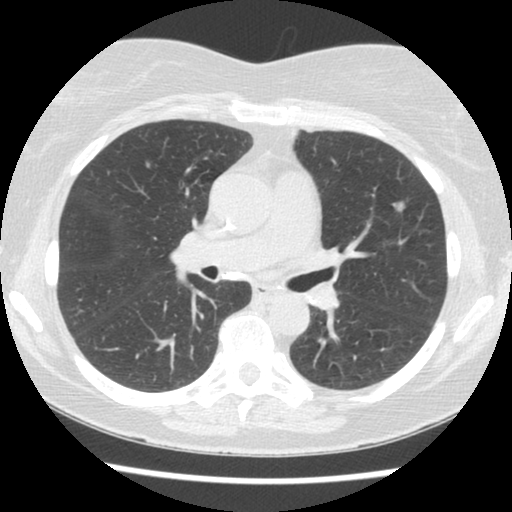
Low-dose screening chest CT, axial slice. Second screening round (one year after baseline). Lung window (W 1500 / L -600 HU). 2.5 mm slice thickness. Standard (soft-tissue) reconstruction kernel (STANDARD). Female, age 60 years at enrolment. Current smoker at enrolment.
Lesion marked by an expert reader, box from (x=376, y=193) to (x=421, y=226) px. The screening reader recorded 3 non-calcified nodules or masses ≥4 mm on this exam (left upper lobe, left upper lobe, right upper lobe); which of them this box marks is not recorded. Official screen result: positive, other.